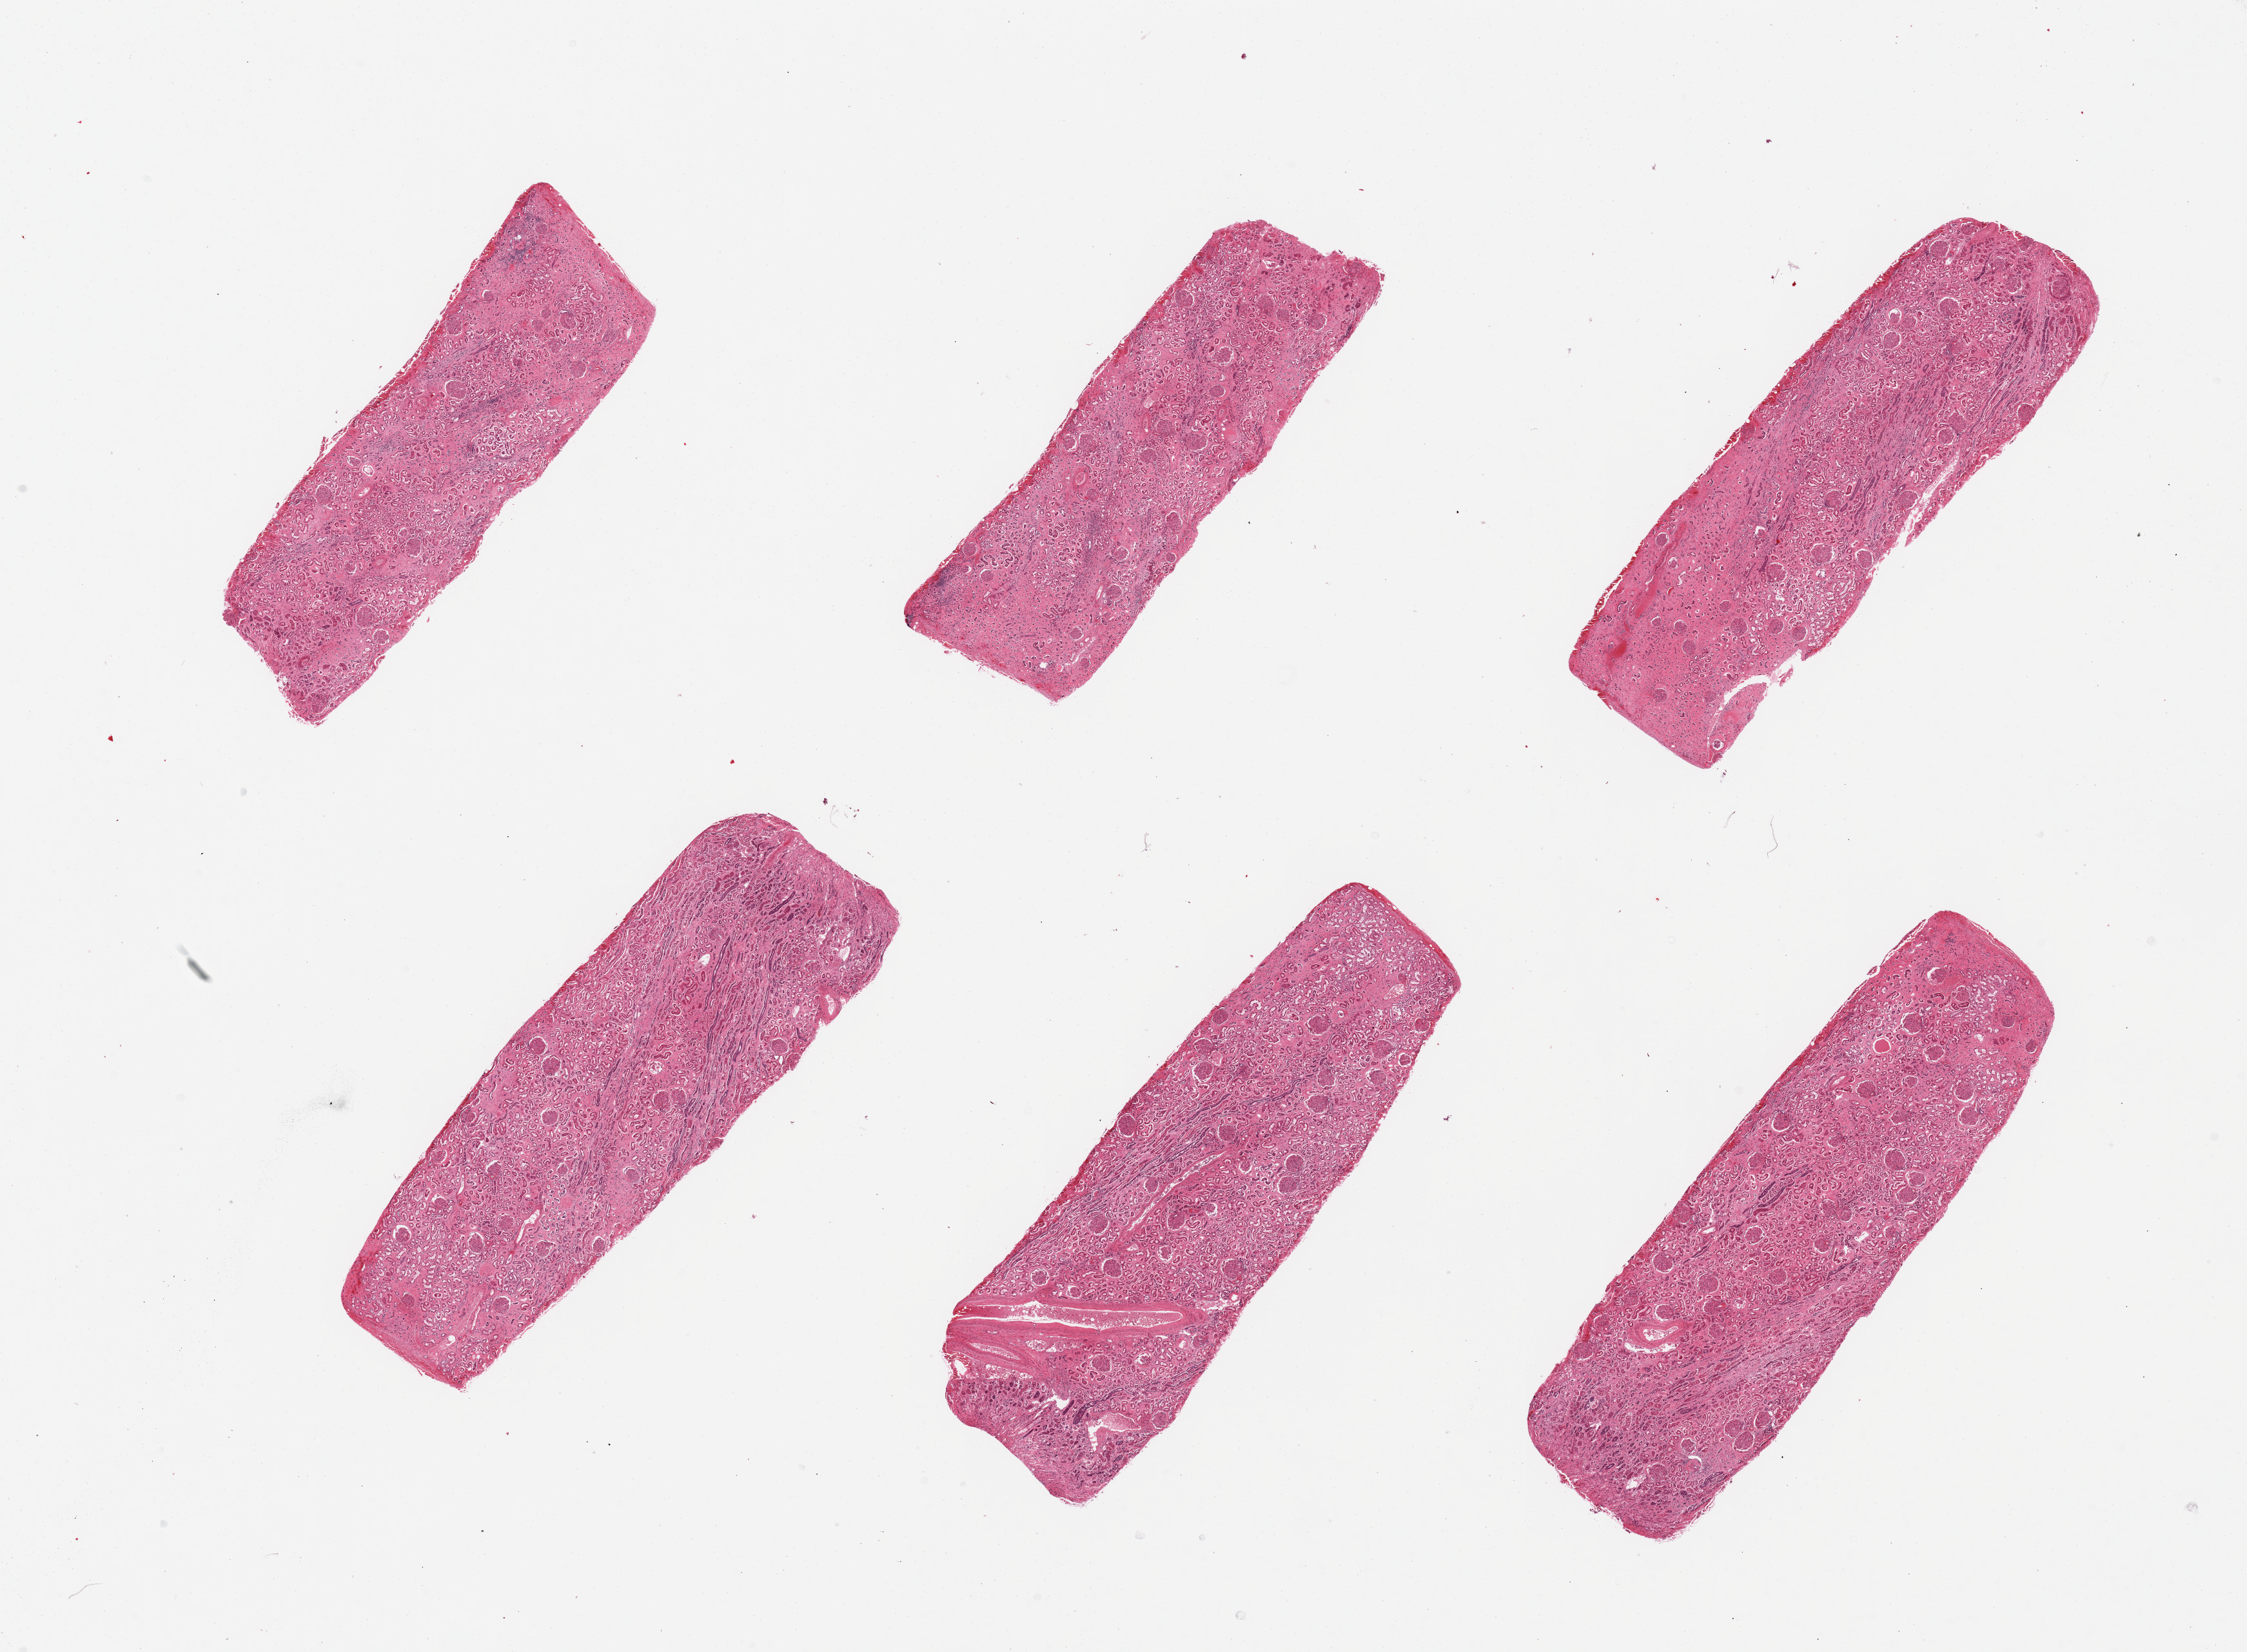
Whole-slide image, haematoxylin and eosin stain, a low-resolution overview of the entire scanned area, about 27.6 x 20.3 mm; PAXgene-fixed, paraffin-embedded tissue; sampled site (target tissue): renal cortex; donor tissue sample. Male donor.
• pathologist's review note for this sample: 6 pieces, hypertensive nephrosclerosis with focal hyalinization of glomeruli, fibrinoid necrosis of arterioles, fibrosis, and patchy inflammation